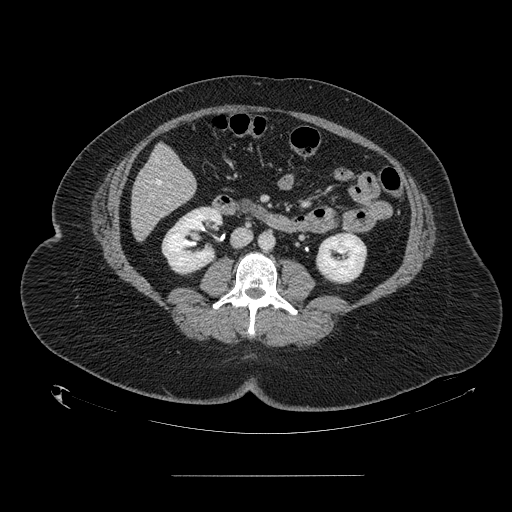
Contrast-enhanced abdominal CT, one axial slice. Position 43 of 164 along the scan axis. Soft-tissue window (W 400 / L 40 HU). 2.5 mm slice thickness. 512 × 512 image matrix, field of view 495 × 495 mm. Female patient, age 52 years. From the clinical record (not read from this slice): diagnosis: colorectal cancer liver metastases, imaged before liver resection; multiple liver metastases: yes; largest metastasis: 3.5 cm; disease in both lobes: no.
Outlined on this slice (outlined manually by an expert reader):
- hepatic veins: bounding box (x1, y1, x2, y2) in pixels: (155, 160, 161, 185)
- liver: (132, 146, 196, 240)